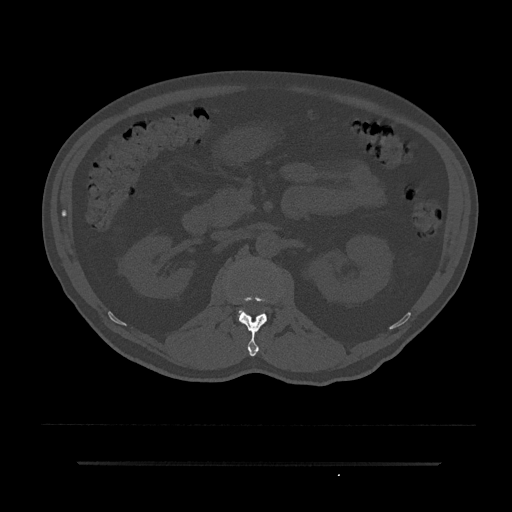
CT including the spine, one axial slice. Reconstruction kernel Br40s/3. Bone window (W 1800 / L 400 HU). 0.5 mm slice thickness. 512 × 512 image matrix, field of view 464 × 464 mm. Male patient, age 59 years. Case-level facts recorded for this patient, not image findings: primary cancer: bile ducts; vertebrae with lytic lesions (as recorded): T10.
Structures marked on this image (semi-automatic segmentation, software-assisted and operator-edited):
- L1 vertebra: bounding box <239,292,278,357> (left, top, right, bottom; pixels)
- L2 vertebra: <239,310,244,316>